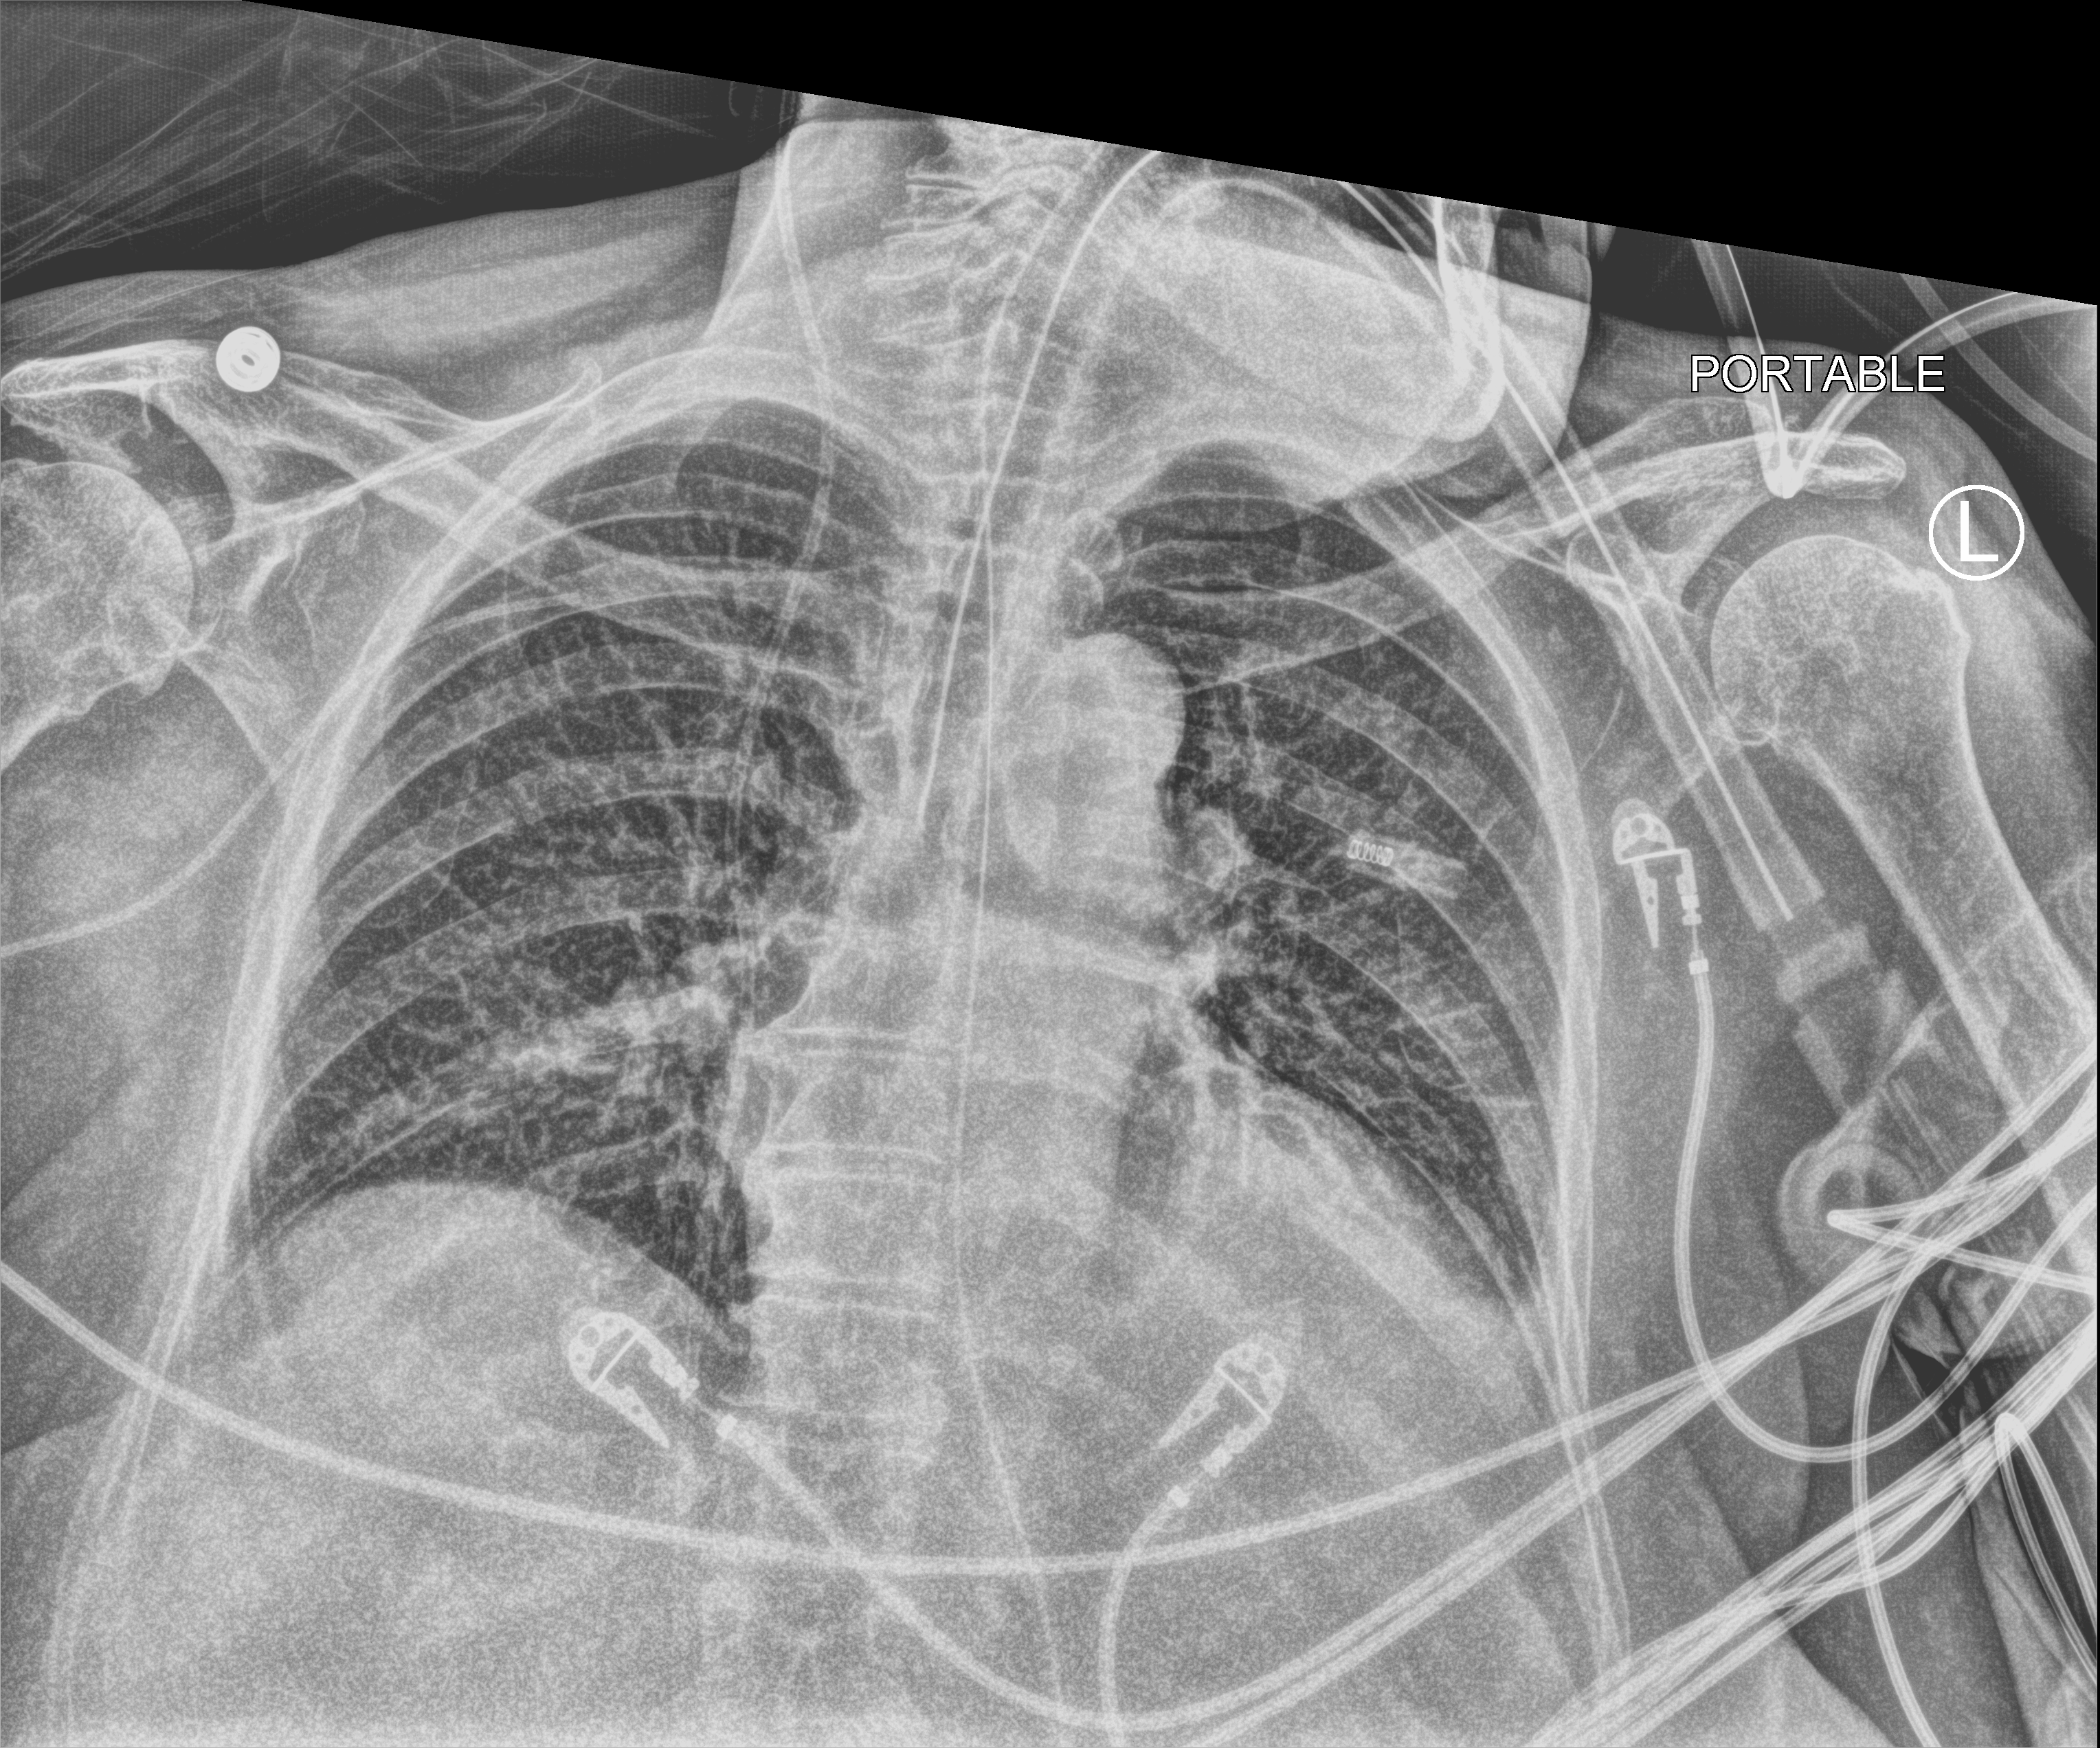
Bedside chest radiograph (computed radiography), anteroposterior (AP) projection. Female patient hospitalised with COVID-19, age 75–90 years.
Hospital-stay facts (about this admission, not read from this image; timing relative to this image not recorded): admitted to intensive care during this hospital stay: yes; hypertension (admission record): yes; mechanically ventilated during this hospital stay: yes.